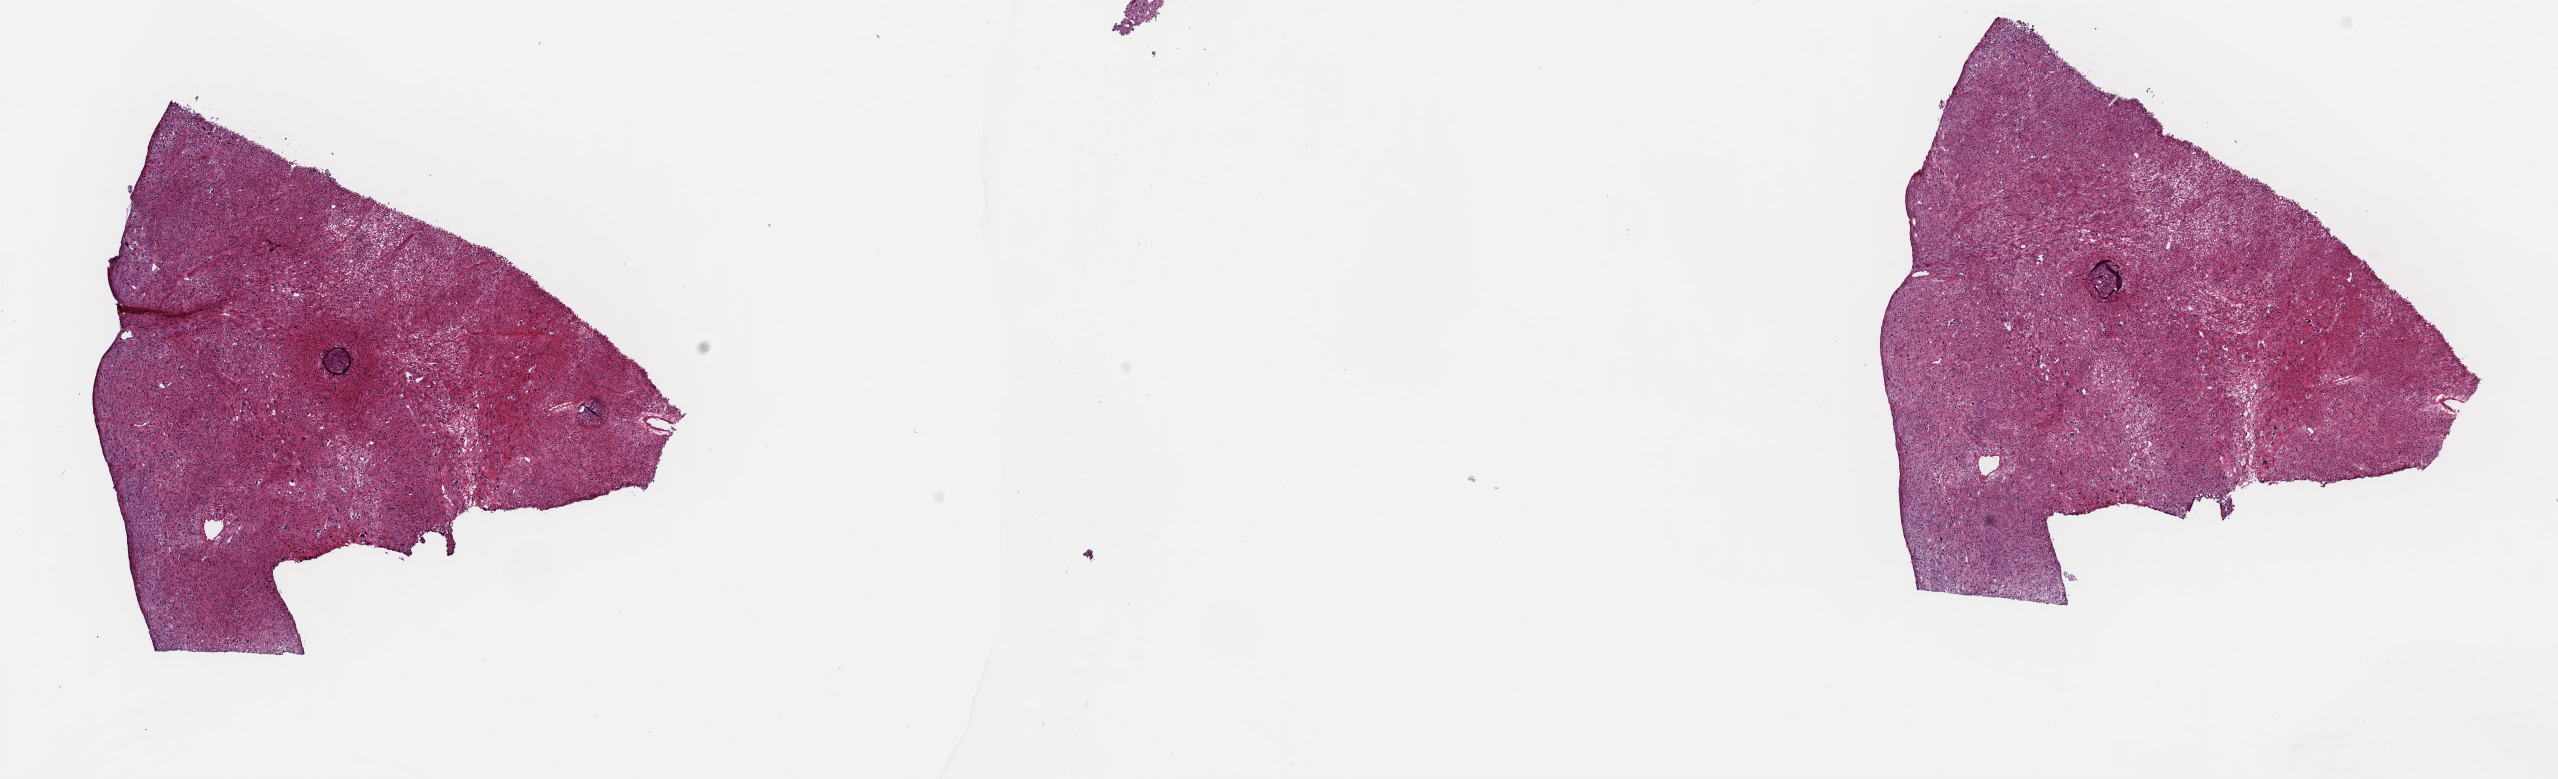
Whole-slide histology image, H&E, shown as a low-resolution overview of the whole scanned area (about 20.2 x 6.2 mm), frozen section from the top of the tissue portion, sample: primary tumour, retroperitoneum and peritoneum. Patient: male, age at initial diagnosis 63 years. Slide review estimates, as recorded: tumour cells 85%, tumour nuclei 100%, normal cells 0%, stromal cells 15%, necrosis 0%. Inflammatory infiltration, as recorded: lymphocyte infiltration 0%, monocyte infiltration 0%, neutrophil infiltration 0%.
* histologic diagnosis: Leiomyosarcoma, NOS